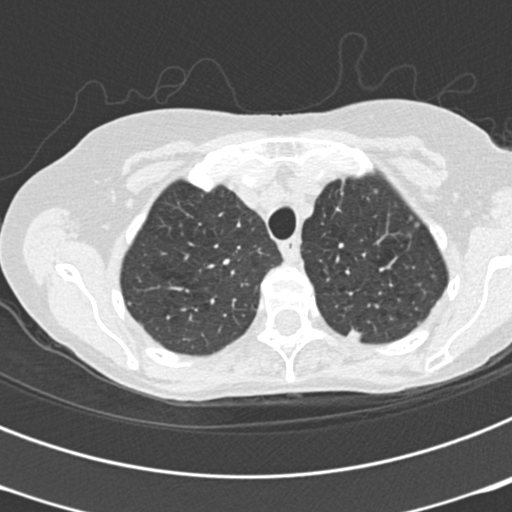
Low-dose screening chest CT, one axial slice; slice 168 of 199 in the series (ordered by position); reconstruction kernel B30f; 120 kVp; lung window (W 1500 / L -600 HU); 2 mm slice thickness; 512 × 512 image matrix.
Structures marked on this image (expert manual segmentation):
- lesion 2 (nodule, upper lobe of left lung): bounding box [x1, y1, x2, y2] px = [348, 329, 361, 341]